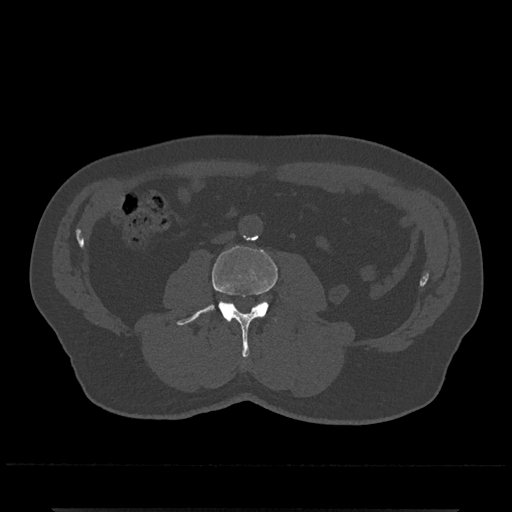
CT including the spine, one axial slice; slice 217 of 797 in the series (ordered by position); bone window (W 1800 / L 400 HU); 0.5 mm slice thickness; 512 × 512 image matrix. Patient: male, 67 years. From the clinical record (not read from this slice): primary cancer: prostate.
Outlined on this slice (semi-automatically segmented with operator editing):
- L3 vertebra: box from (x=177, y=245) to (x=278, y=358) px